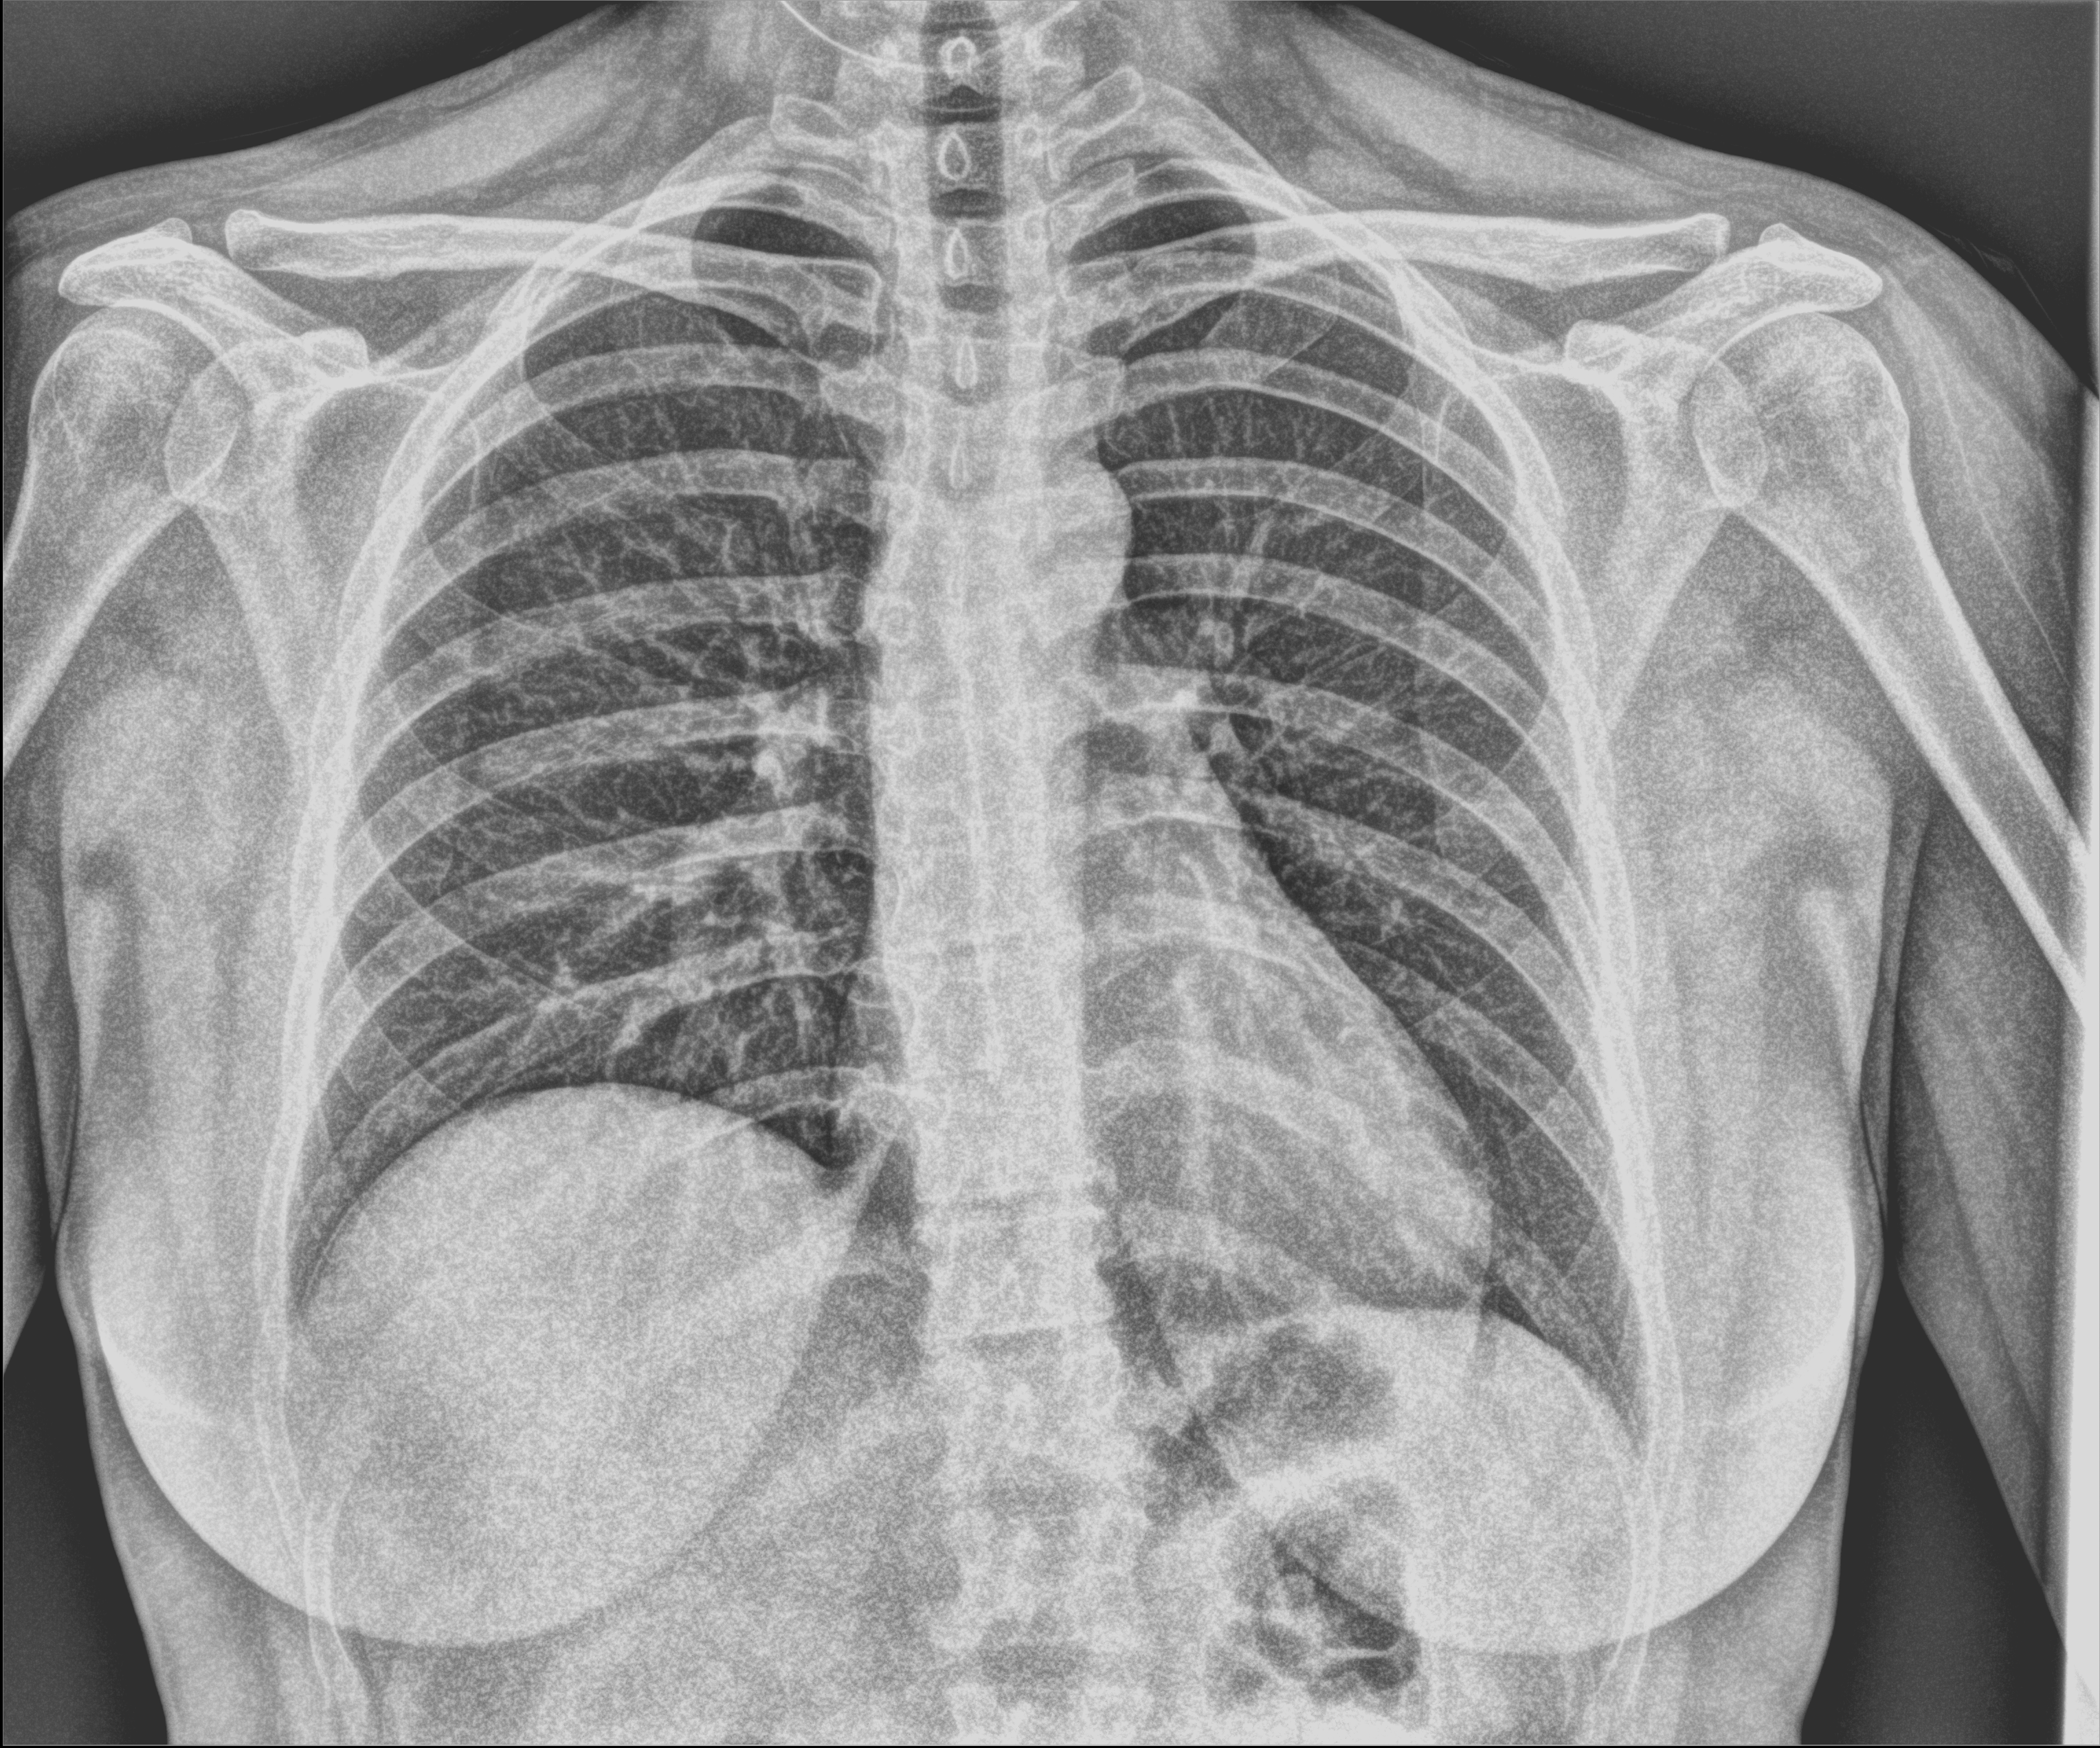
Bedside chest radiograph (computed radiography); anteroposterior (AP) projection. Patient hospitalised with COVID-19; female, aged 18–59 years.
From the hospital-stay record, not from the radiograph (when in the stay this image was taken is not recorded):
- mechanically ventilated during this hospital stay: no